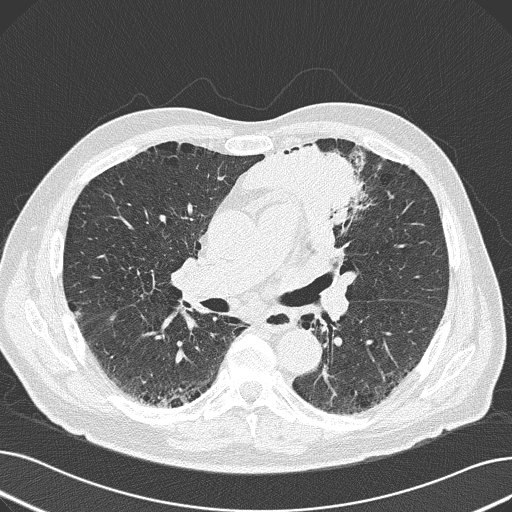
Axial slice from a low-dose chest CT screening exam, baseline annual screen, lung window (W 1500 / L -600 HU), 2 mm slice thickness, 512 × 512 image matrix. Male, age 69 years at enrolment.
- Expert reader's lesion annotation, bounding box [x1, y1, x2, y2] px = [239, 128, 387, 248].
- Screening reader's record for this exam (one nodule recorded; not confirmed to be the boxed lesion): non-calcified nodule or mass ≥4 mm, left upper lobe, 6 × 10 mm, spiculated (stellate) margins, soft tissue attenuation.